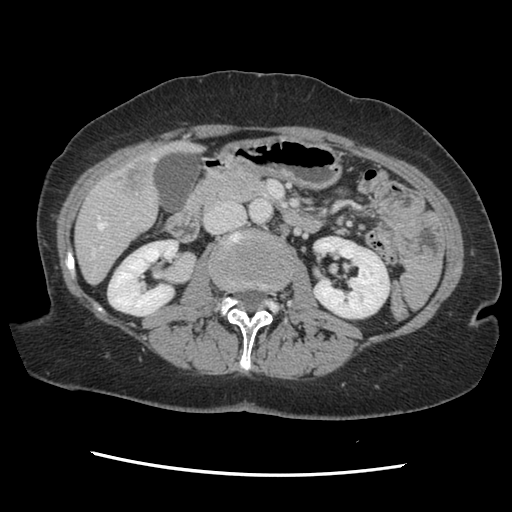
Contrast-enhanced abdominal CT, one axial slice; position 55 of 141 along the scan axis; soft-tissue window (W 400 / L 40 HU); 2.5 mm slice thickness; 512 × 512 image matrix, field of view 330 × 330 mm. Female patient, age 61 years. Case-level facts recorded for this patient, not image findings: diagnosis: colorectal cancer liver metastases, imaged before liver resection; multiple liver metastases: no; largest metastasis: 2.4 cm; chemotherapy before resection: no.
Outlined on this slice (manually delineated by an expert):
- hepatic veins: bounding box <92,157,156,259> (left, top, right, bottom; pixels)
- liver: <76,142,197,282>
- planned liver remnant (the part of the liver to remain after resection): <76,194,159,282>
- portal vein (with intrahepatic branches): <101,223,129,248>
- liver metastasis: <115,159,153,197>